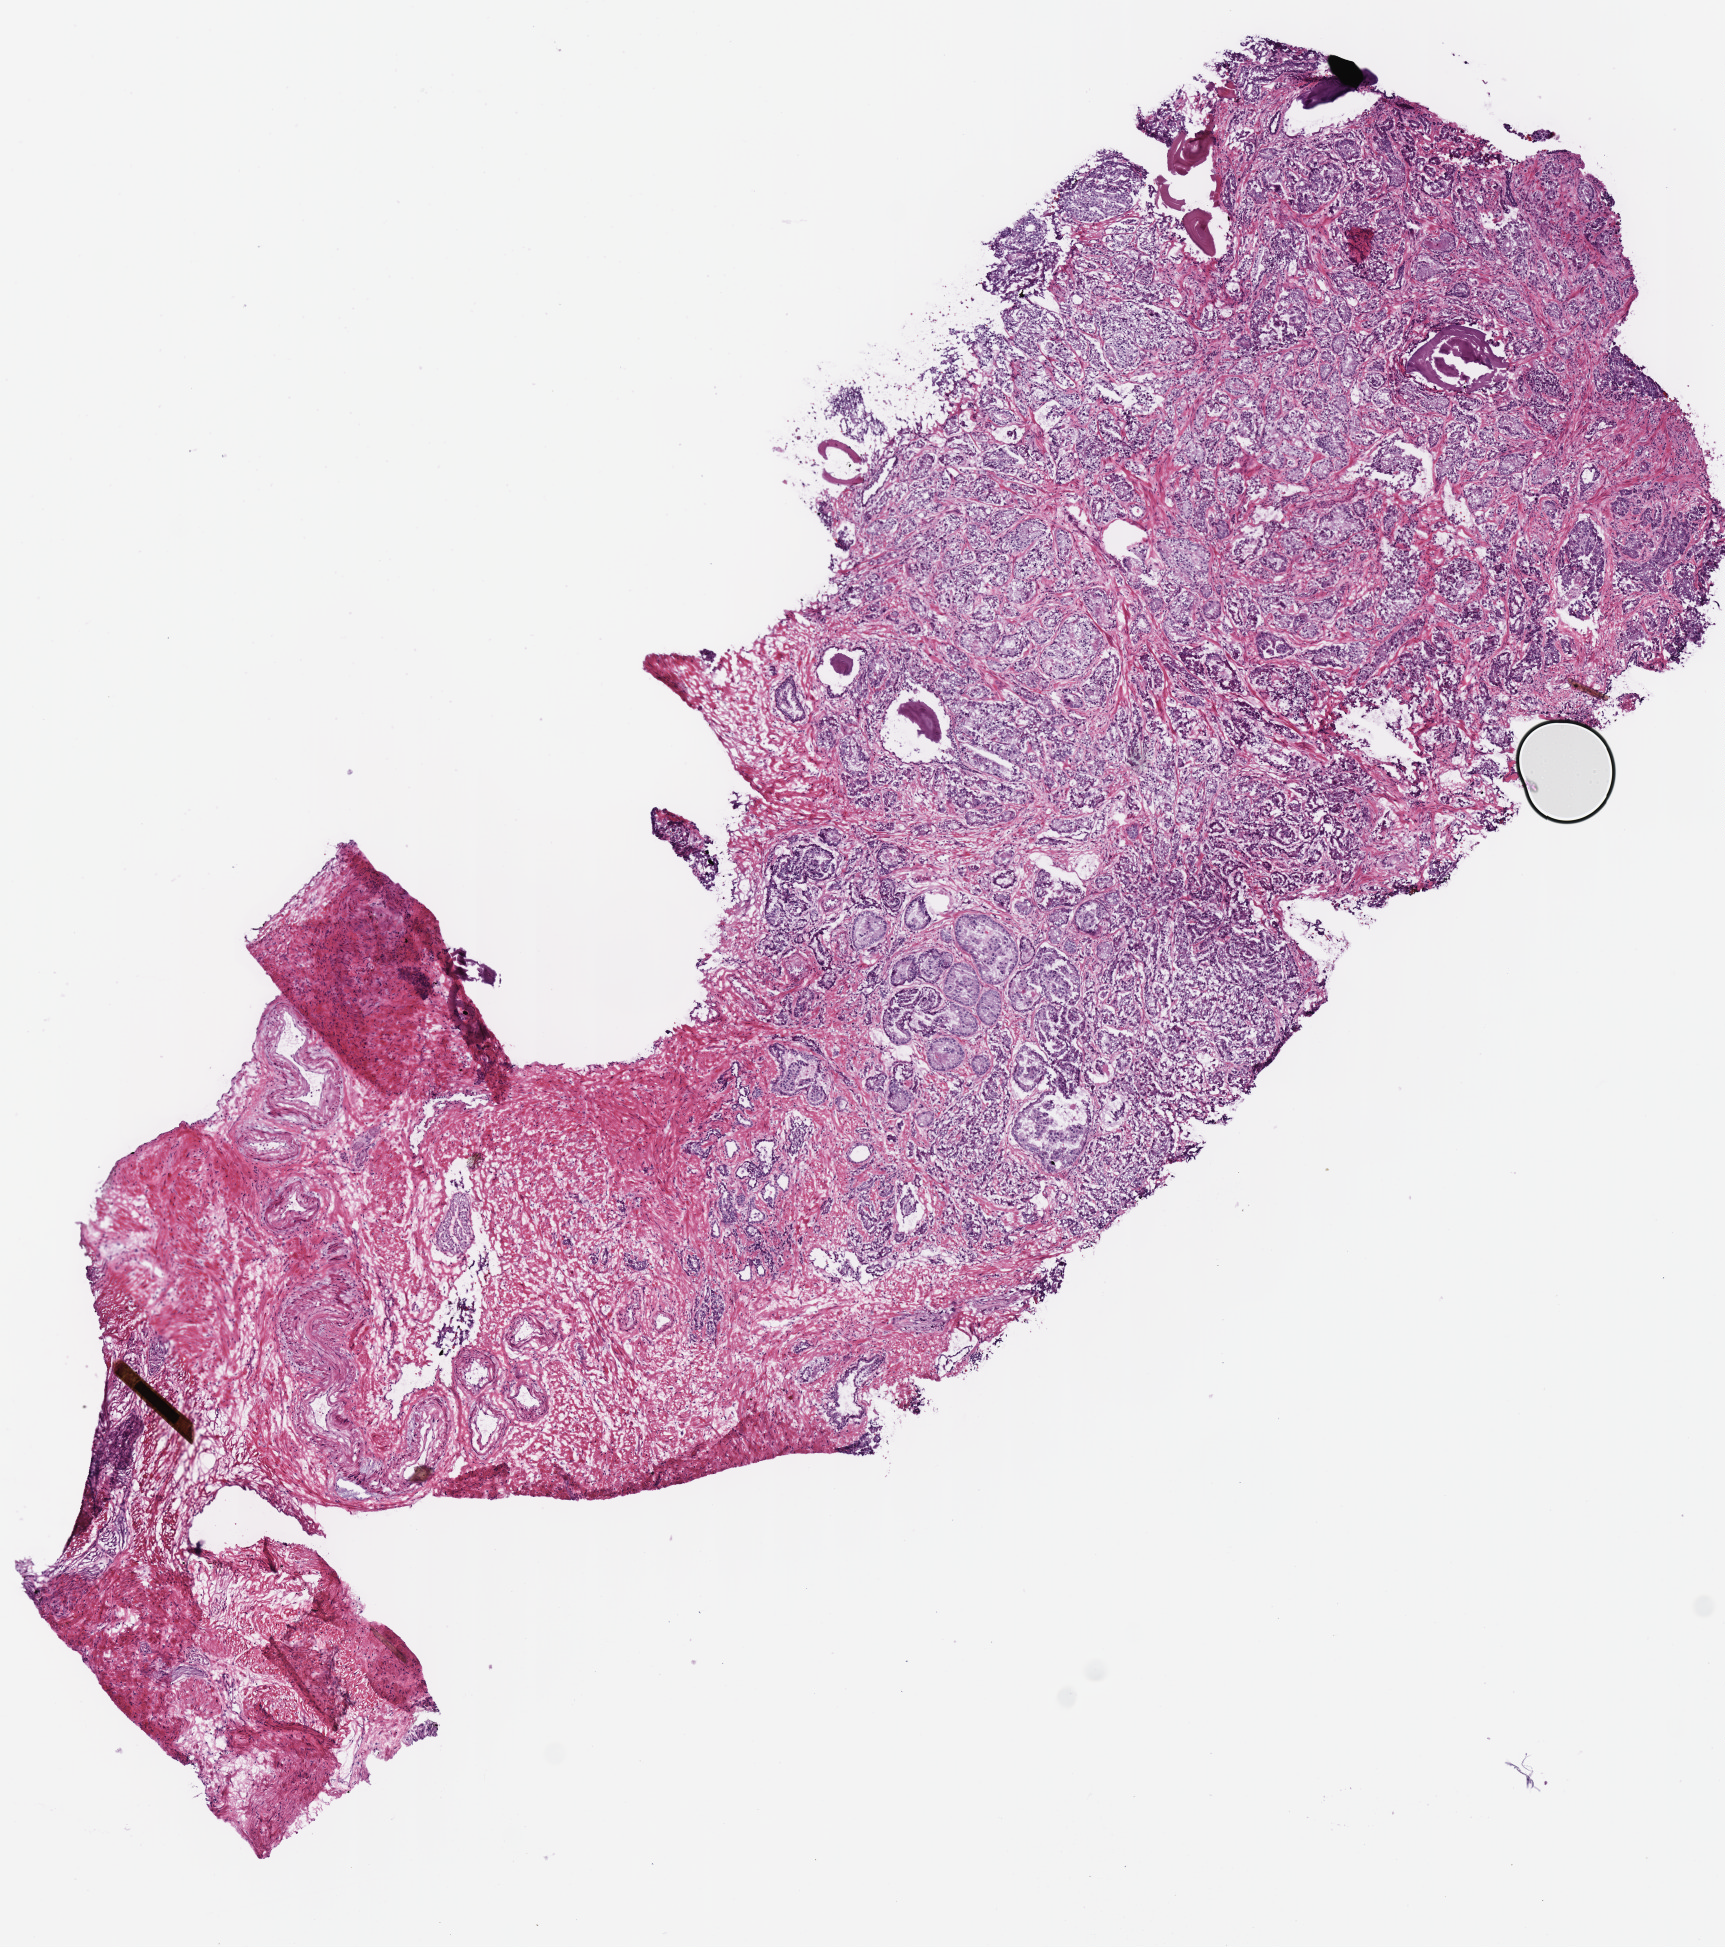
Digitized H&E-stained tissue section (whole slide) — a low-resolution overview of the entire scanned area, about 6.8 x 7.7 mm, frozen section from the top of the tissue portion, primary tumour sample from the prostate. Male patient; age at initial diagnosis 58 years. Gleason score: 7 (3+4). Pathologist review of this section (percent, as recorded): tumour cells 60%, tumour nuclei 60%, normal cells 5%, stromal cells 35%, necrosis 0%.
• pathologic diagnosis: Adenocarcinoma, NOS (prostate gland)